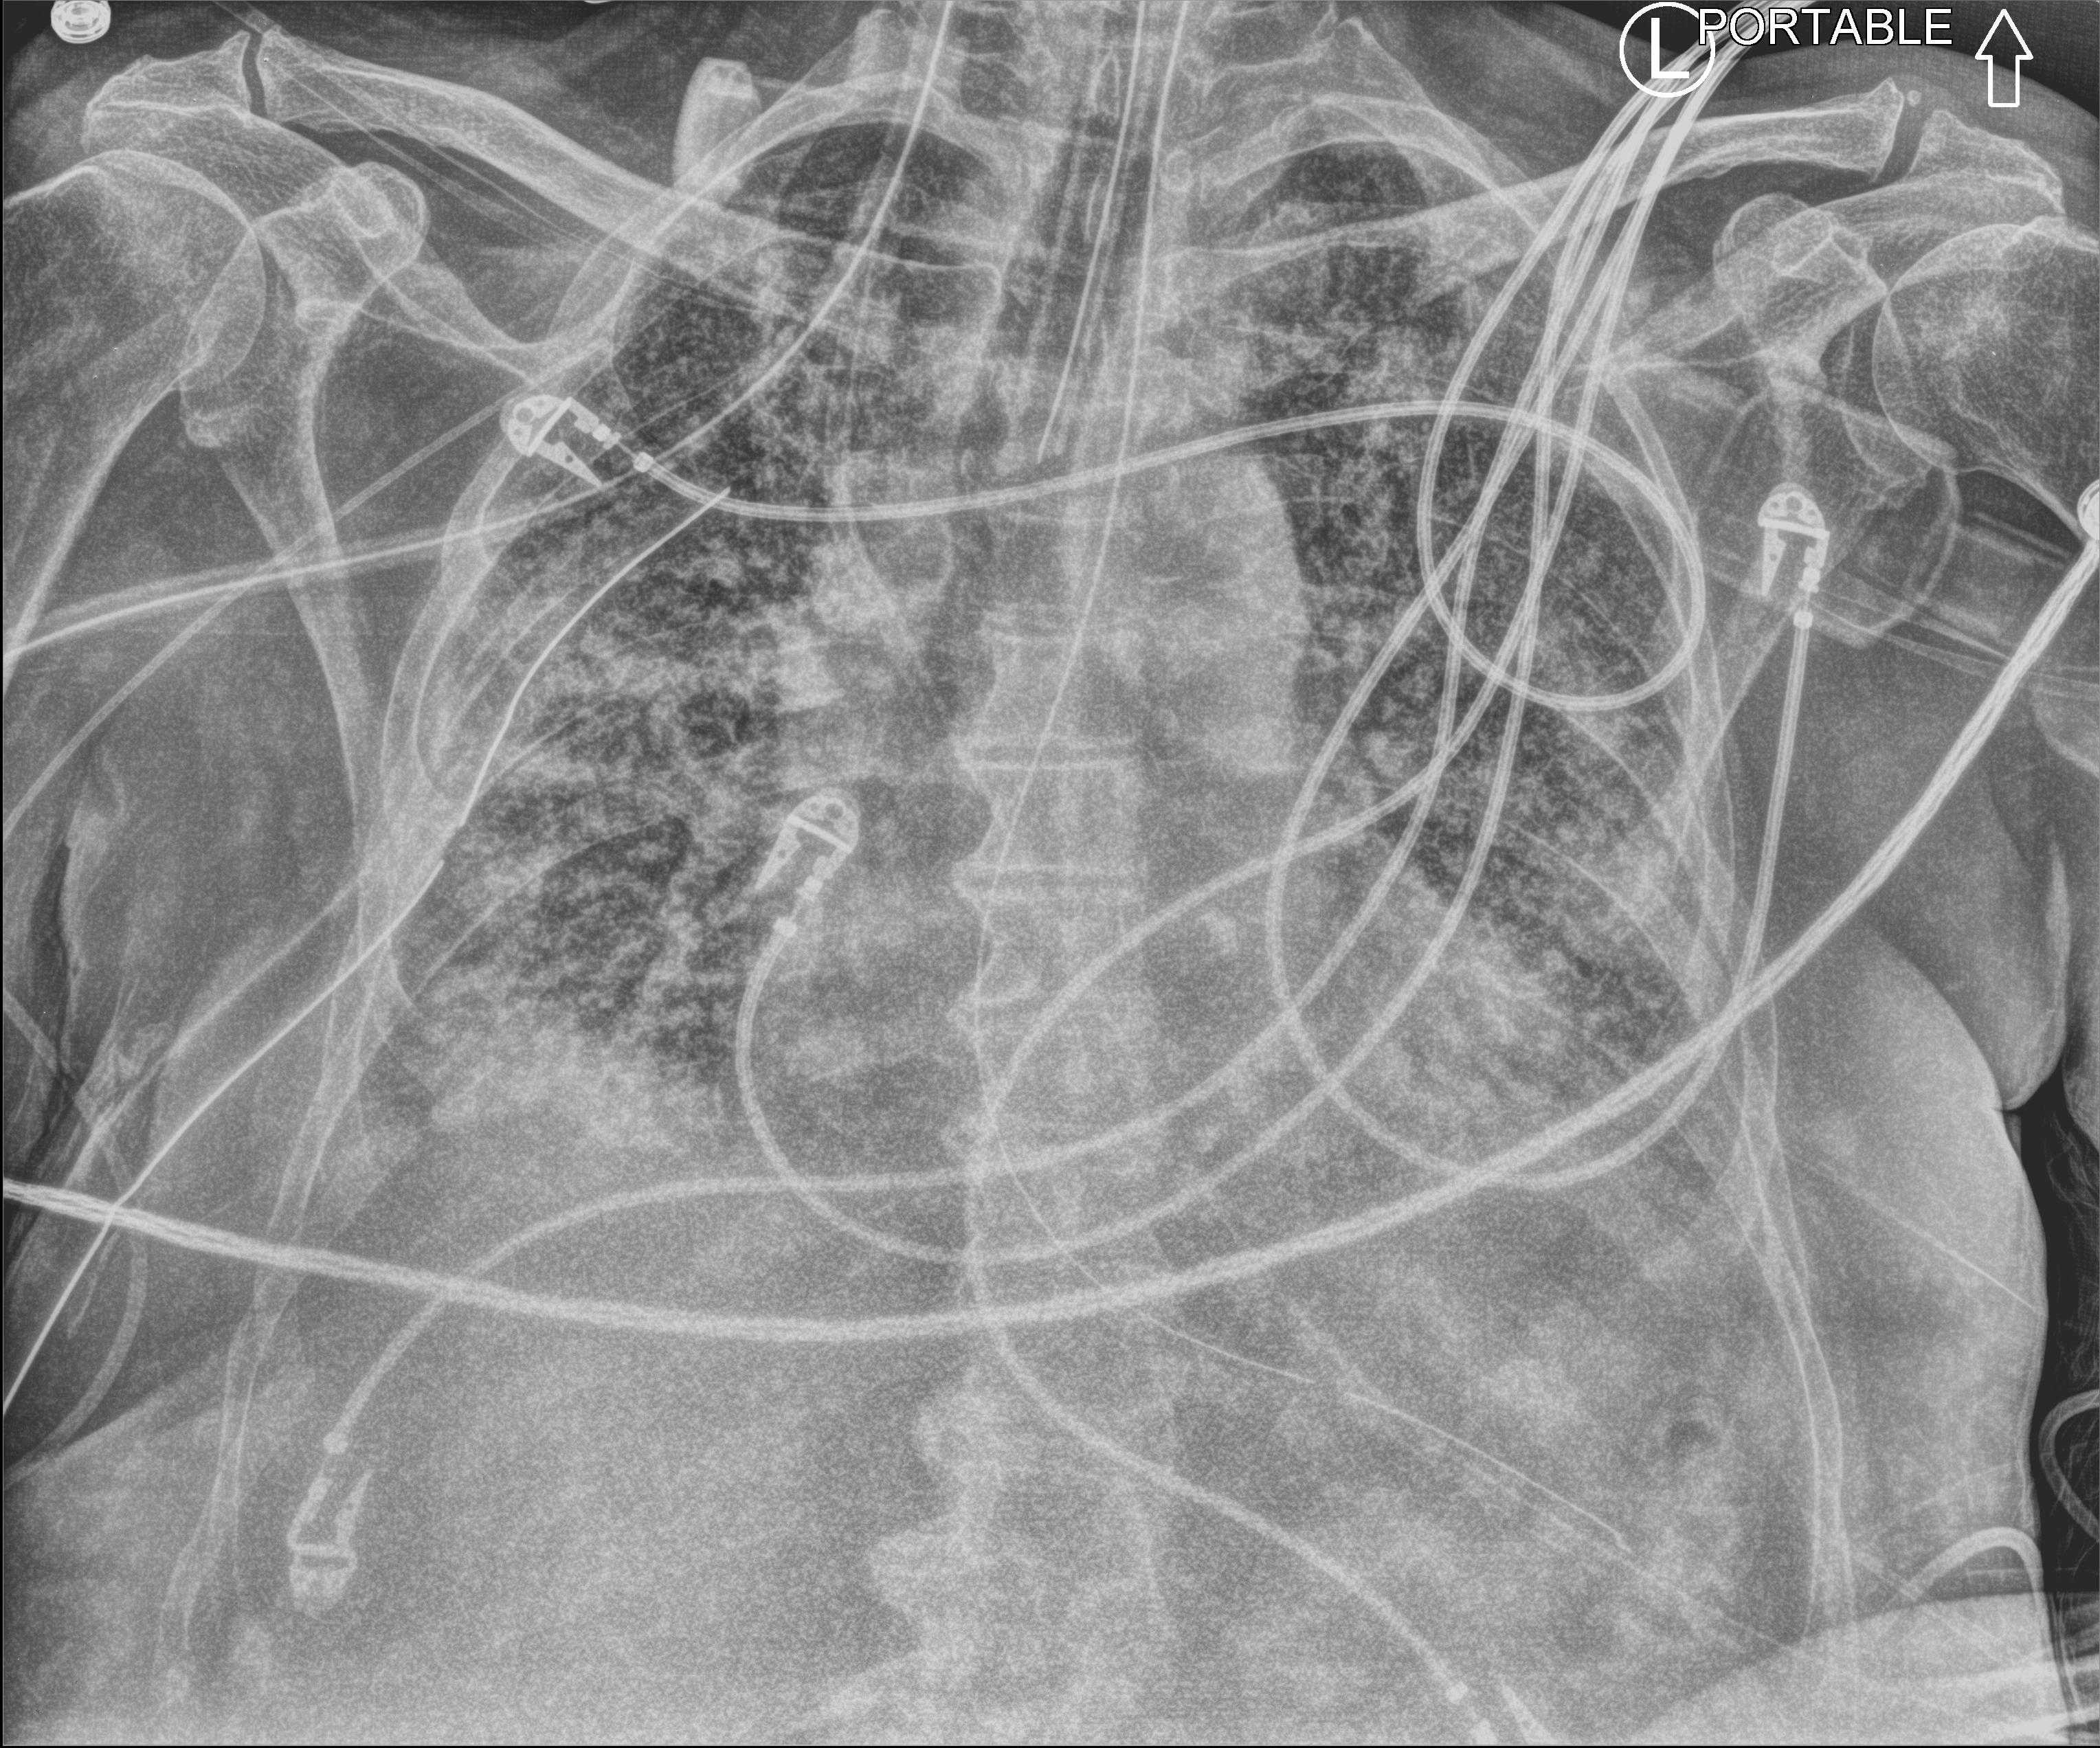
Chest X-ray (portable); anteroposterior (AP) projection. Patient hospitalised with COVID-19; male, aged 75–90 years.
From the hospital-stay record, not from the radiograph (when in the stay this image was taken is not recorded): admitted to intensive care during this hospital stay: yes; other chronic lung disease (admission record): no; mechanically ventilated during this hospital stay: yes.